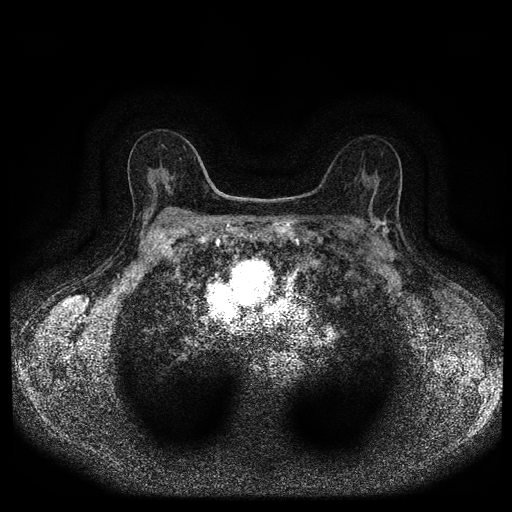
Breast MRI (dynamic contrast-enhanced, multi-phase), one axial slice; slice 60 of 116 in the series (ordered by position); dynamic contrast-enhanced series, time point 2 of 5 at this slice position (early post-contrast); 1.5 T; TE 2.7 ms, TR 5.4 ms; 2 mm slice thickness; 512 × 512 image matrix. Female patient, age 63 years.
Outlined on this slice (semi-automatically segmented with operator editing):
- breast lesion (labelled 'tumour' in the annotation; benign lesions carry a separate 'benign' label): box from (x=370, y=218) to (x=394, y=239) px